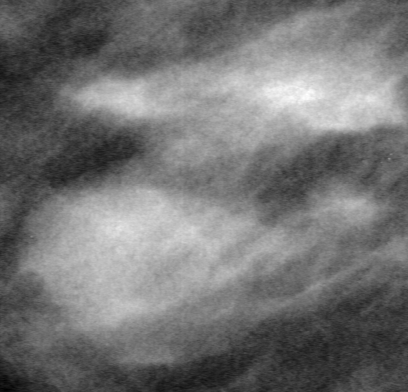
Cropped region of a digitized screen-film mammogram centred on a radiologist-marked abnormality; left breast; MLO view.
Marked abnormality: mass, shape lobulated, margins ill defined; BI-RADS assessment category 4; subtlety rating 5 on a 1 (subtle) to 5 (obvious) scale; pathology (as recorded): benign.